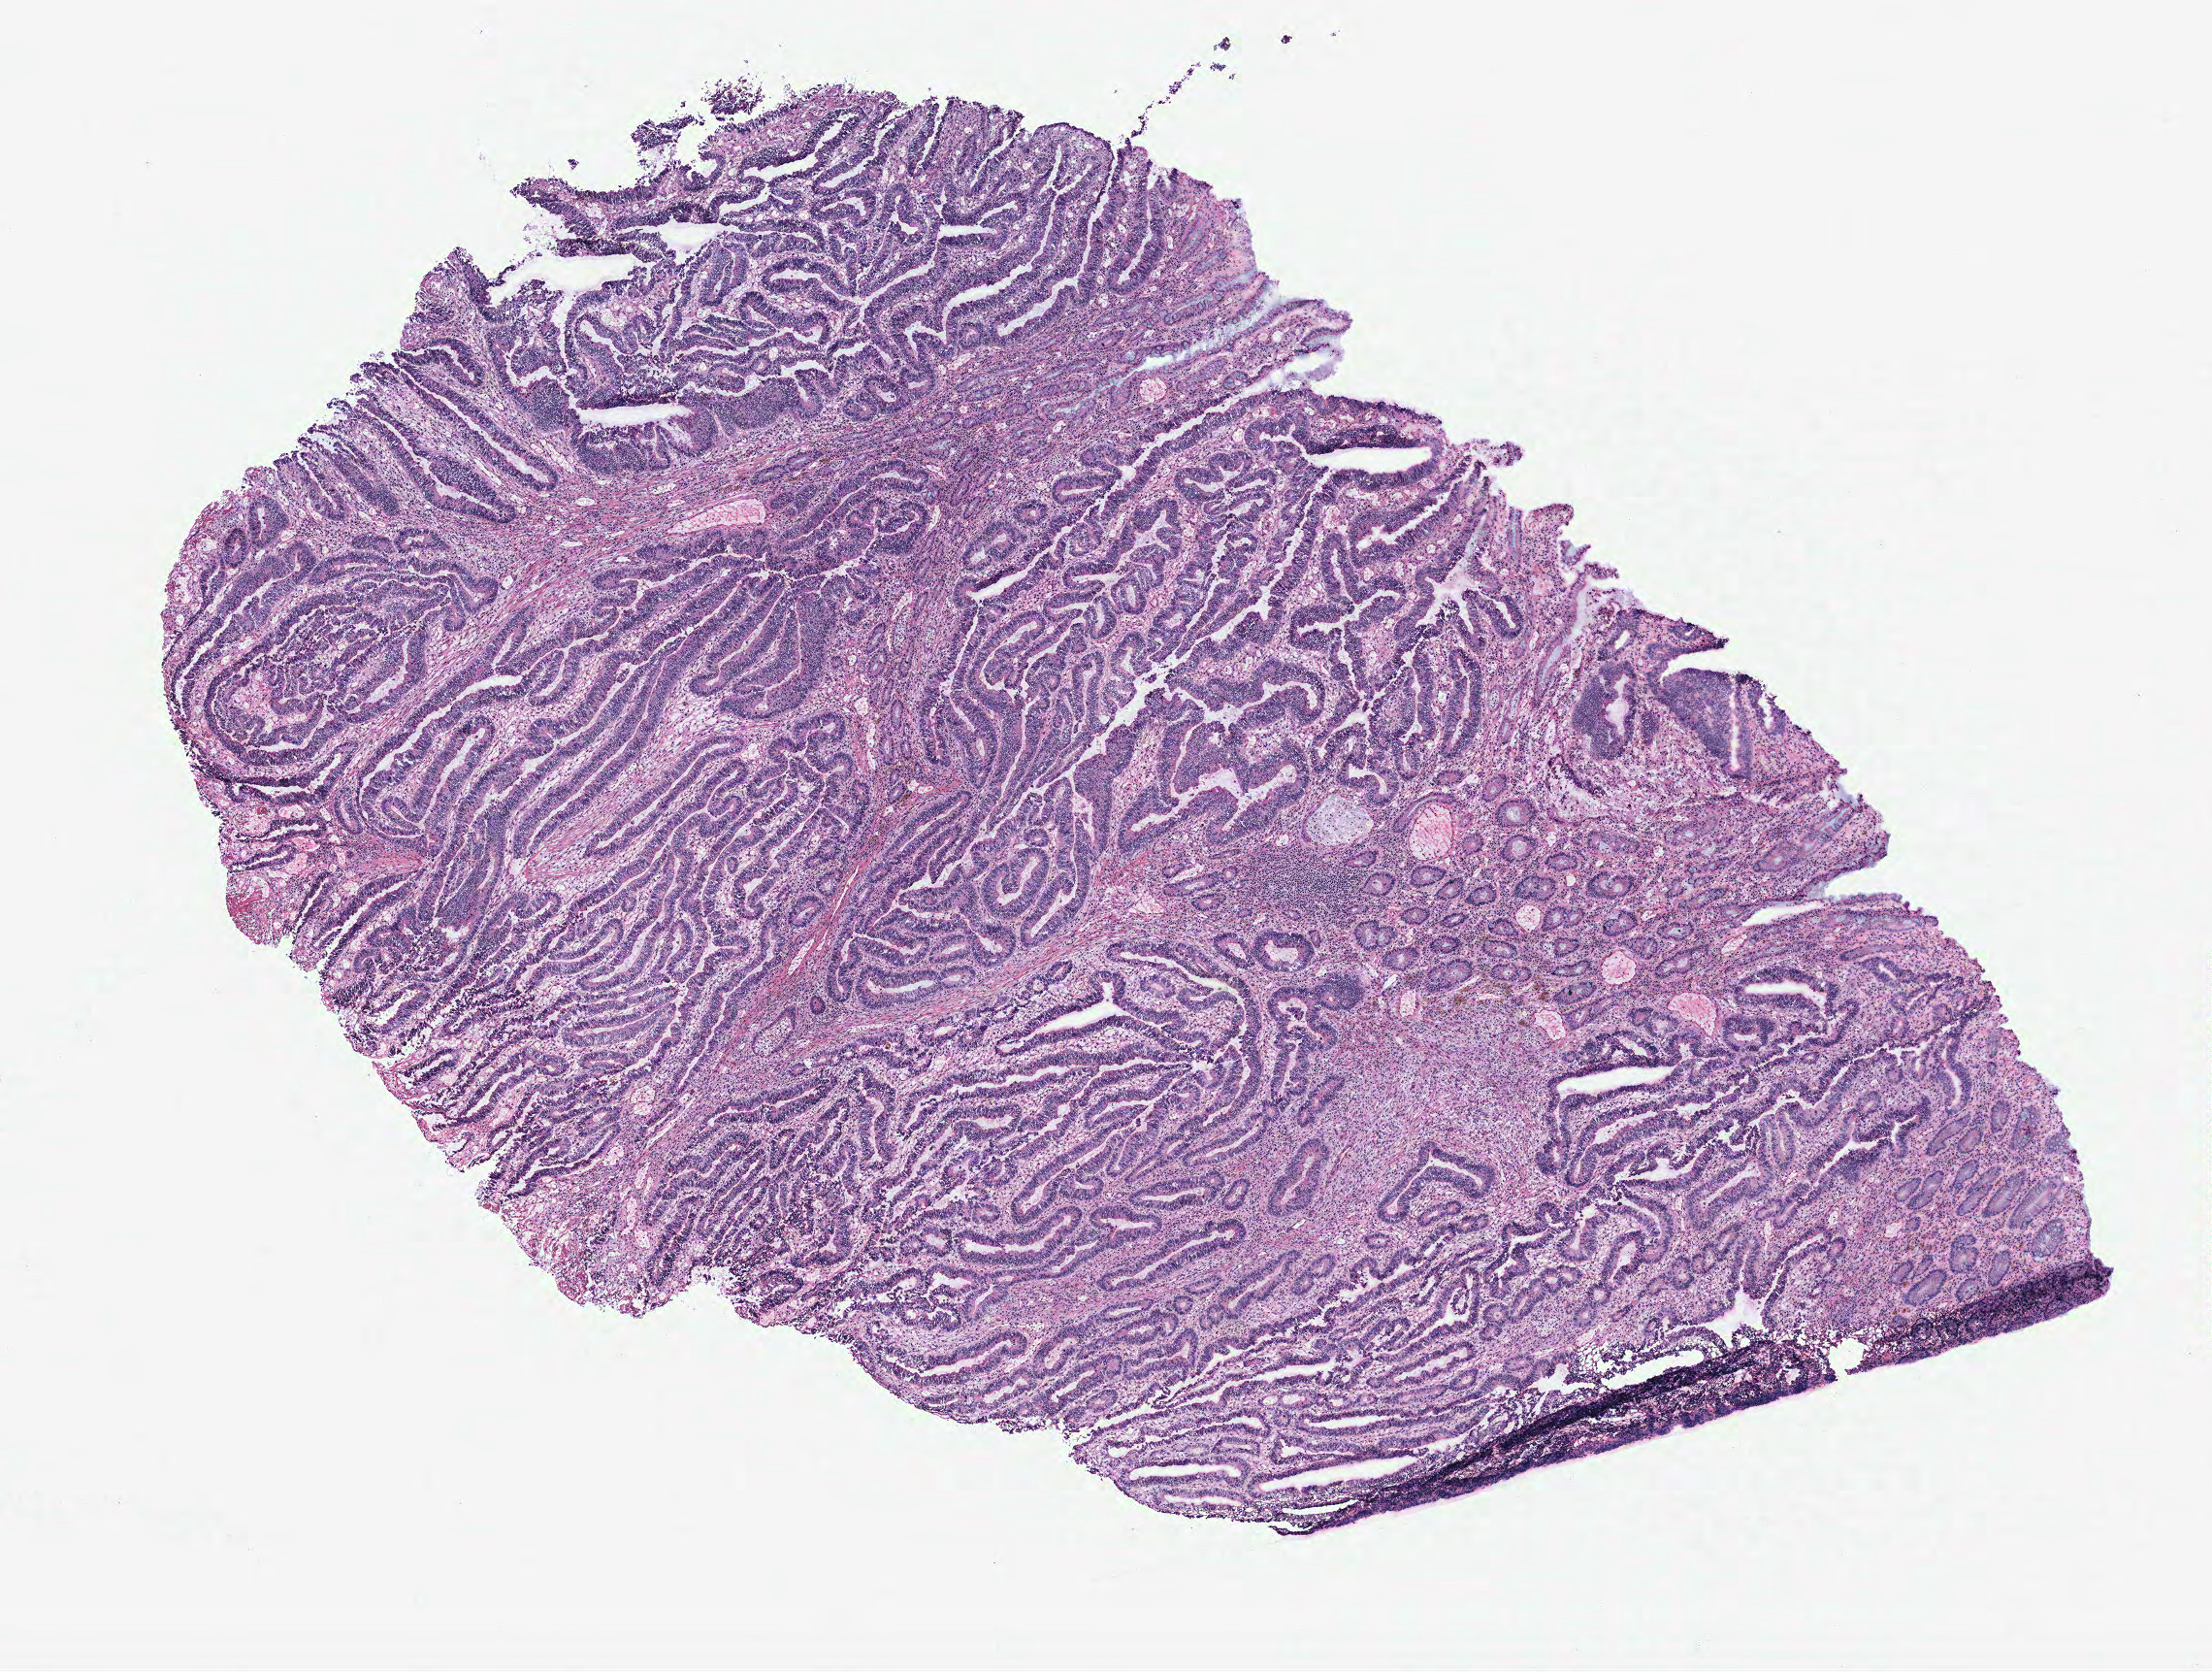
Whole-slide histology image, H&E — low-resolution overview of the scanned area, about 9.1 x 6.9 mm (from a 40x scan); colon, normal (non-tumour) tissue. 70-year-old female patient.
- this section: normal (non-tumour) tissue from the same patient
- patient diagnosis: Adenocarcinoma, NOS